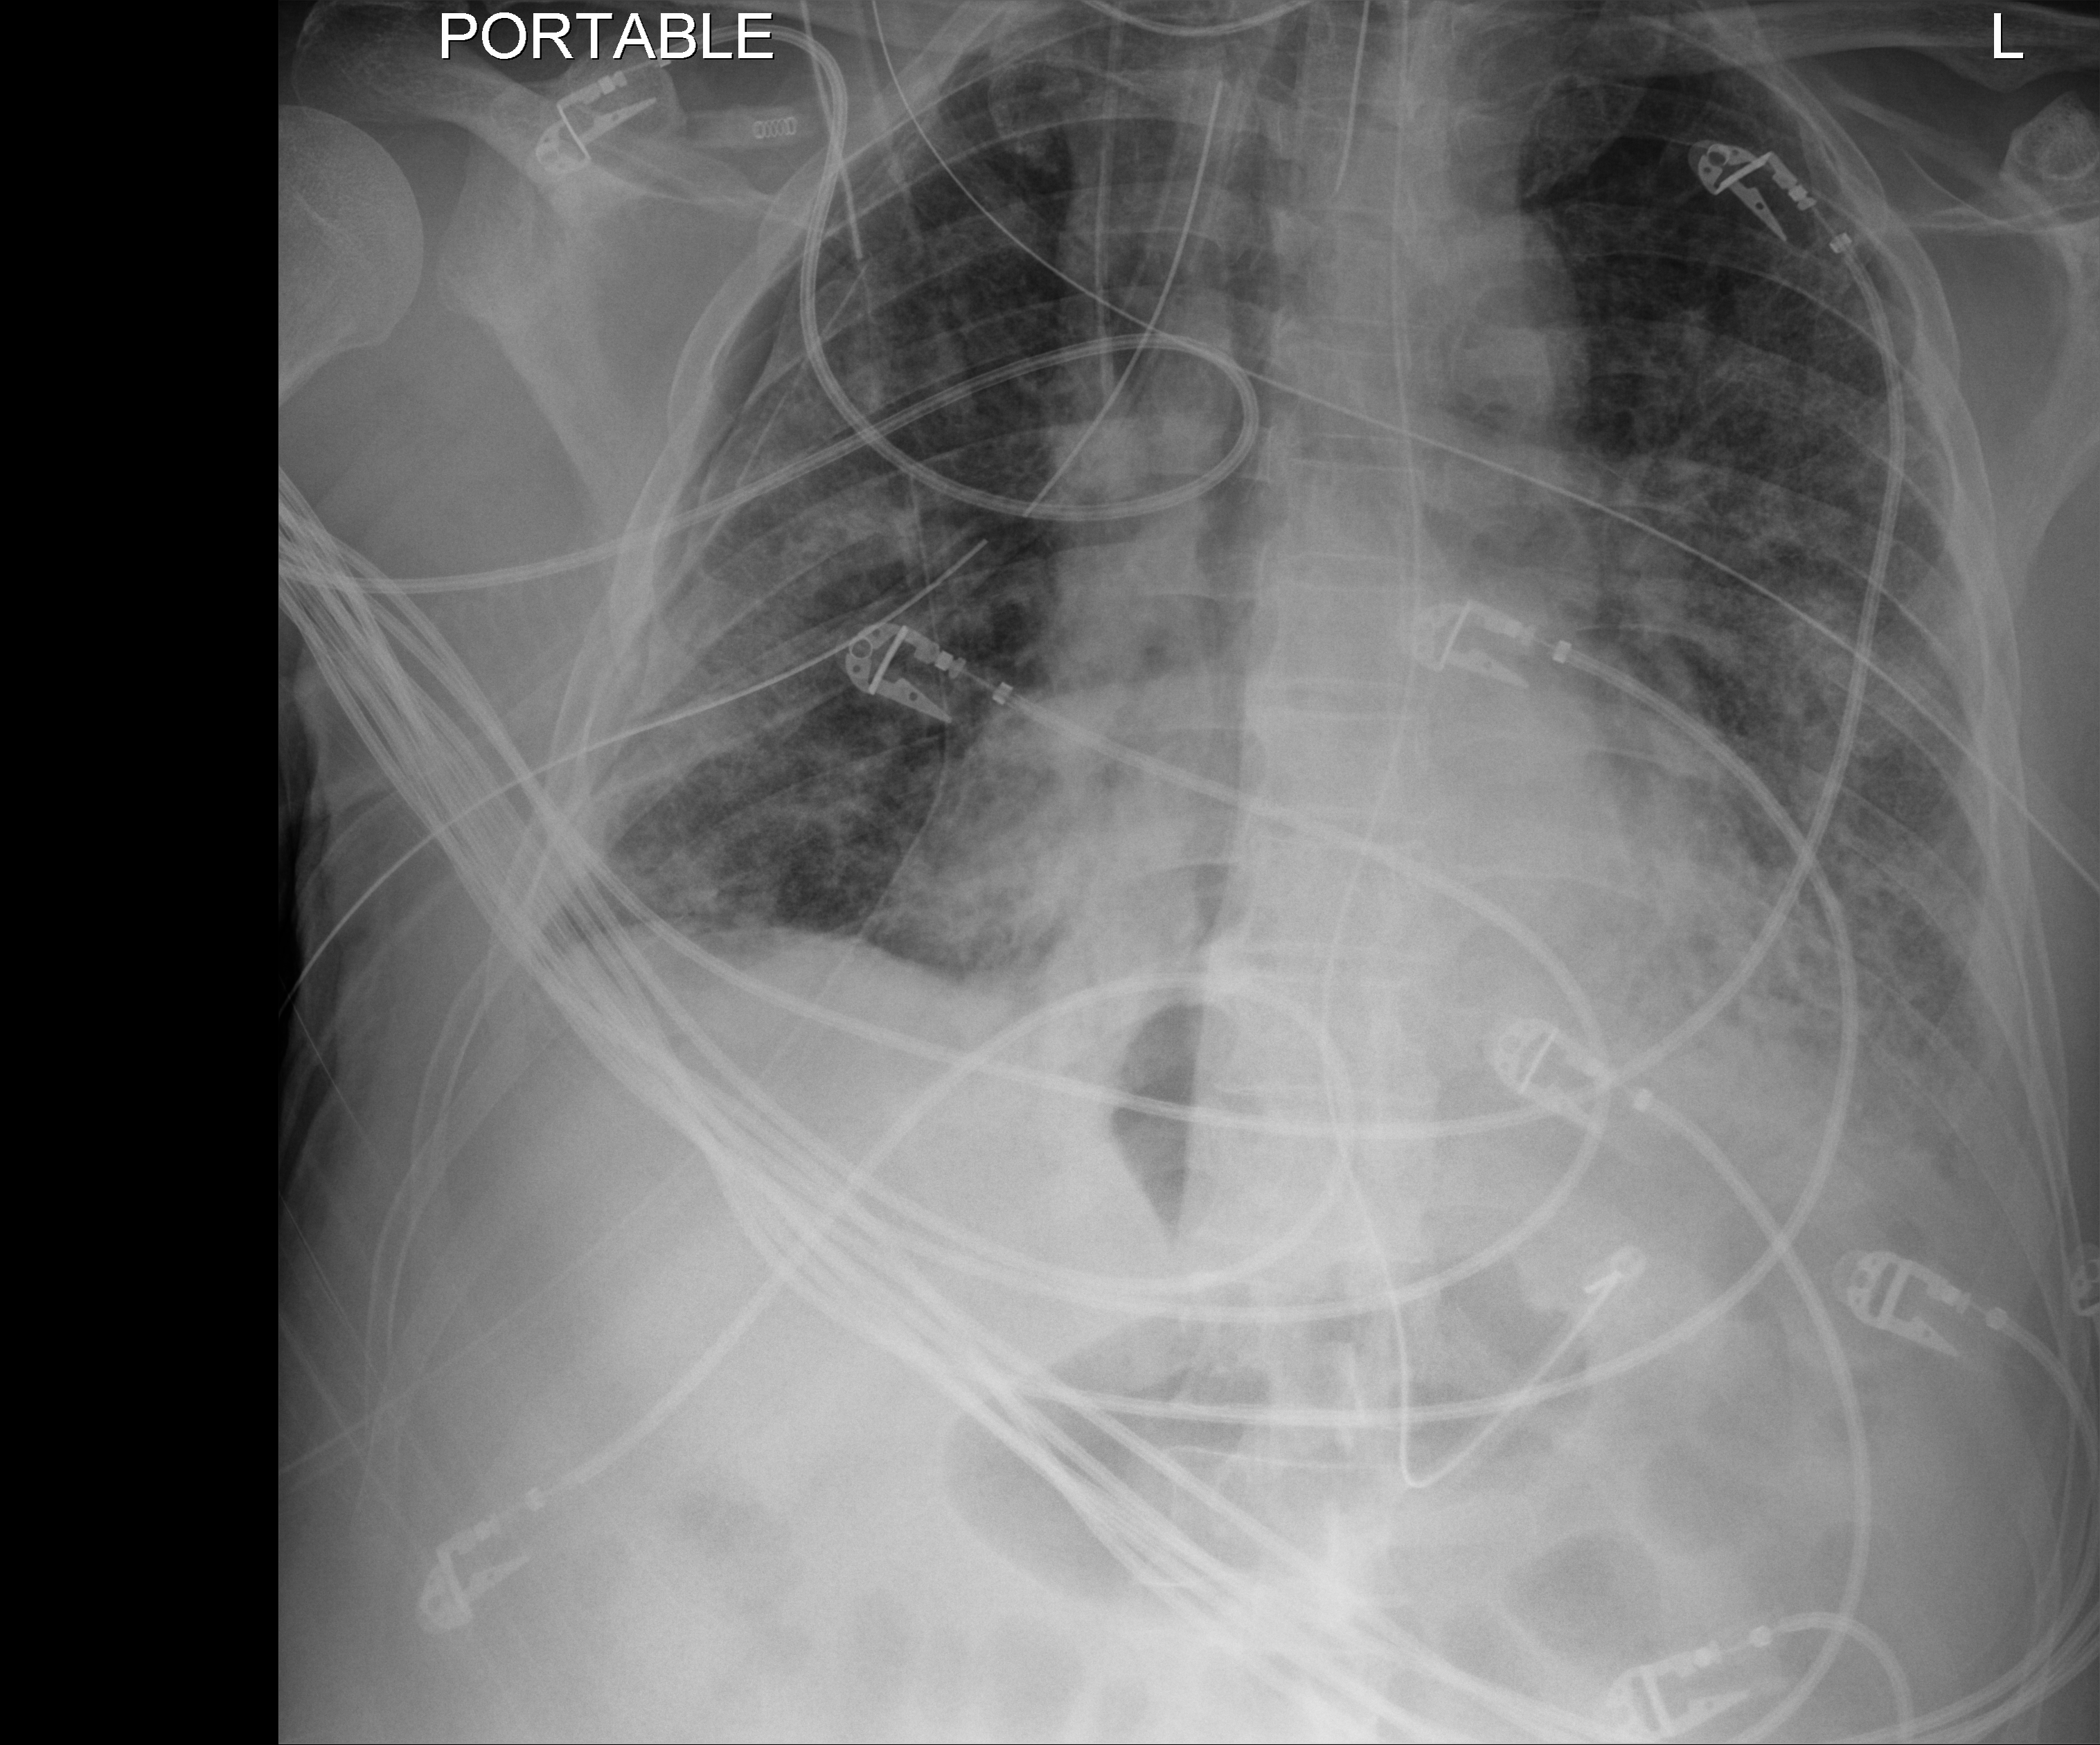
Bedside chest radiograph (digital radiography), anteroposterior (AP) projection. Patient hospitalised with COVID-19; male, aged 60–74 years.
Admission-level facts for this patient (not findings on this image; timing relative to this image not recorded): length of hospital stay: 37 days; COPD (admission record): no.